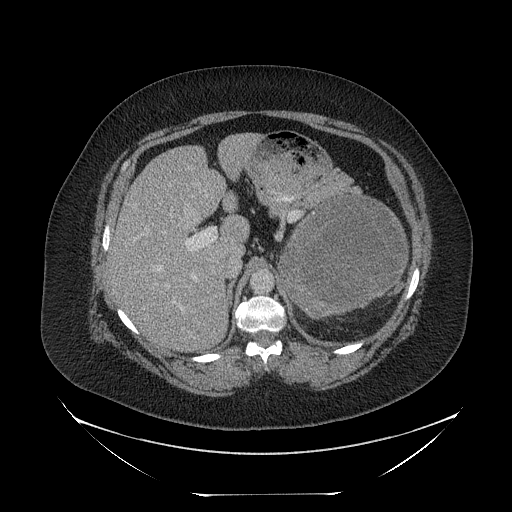
Contrast-enhanced abdominal CT, one axial slice. Slice 155 of 205 in the series (ordered by position). Reconstruction kernel STANDARD. 120 kVp. Soft-tissue window (W 400 / L 40 HU). 2.5 mm slice thickness. 512 × 512 image matrix, field of view 500 × 500 mm. Patient: female, 53 years. Case-level facts recorded for this patient, not image findings: diagnosis: adrenocortical carcinoma; tumour side: left adrenal; tumour size at pathology: 17 cm; Ki-67 index: 20 %.
Structures marked on this image (semi-automatic segmentation, software-assisted and operator-edited):
- mass: bounding box (x1, y1, x2, y2) in pixels: (282, 195, 405, 317)